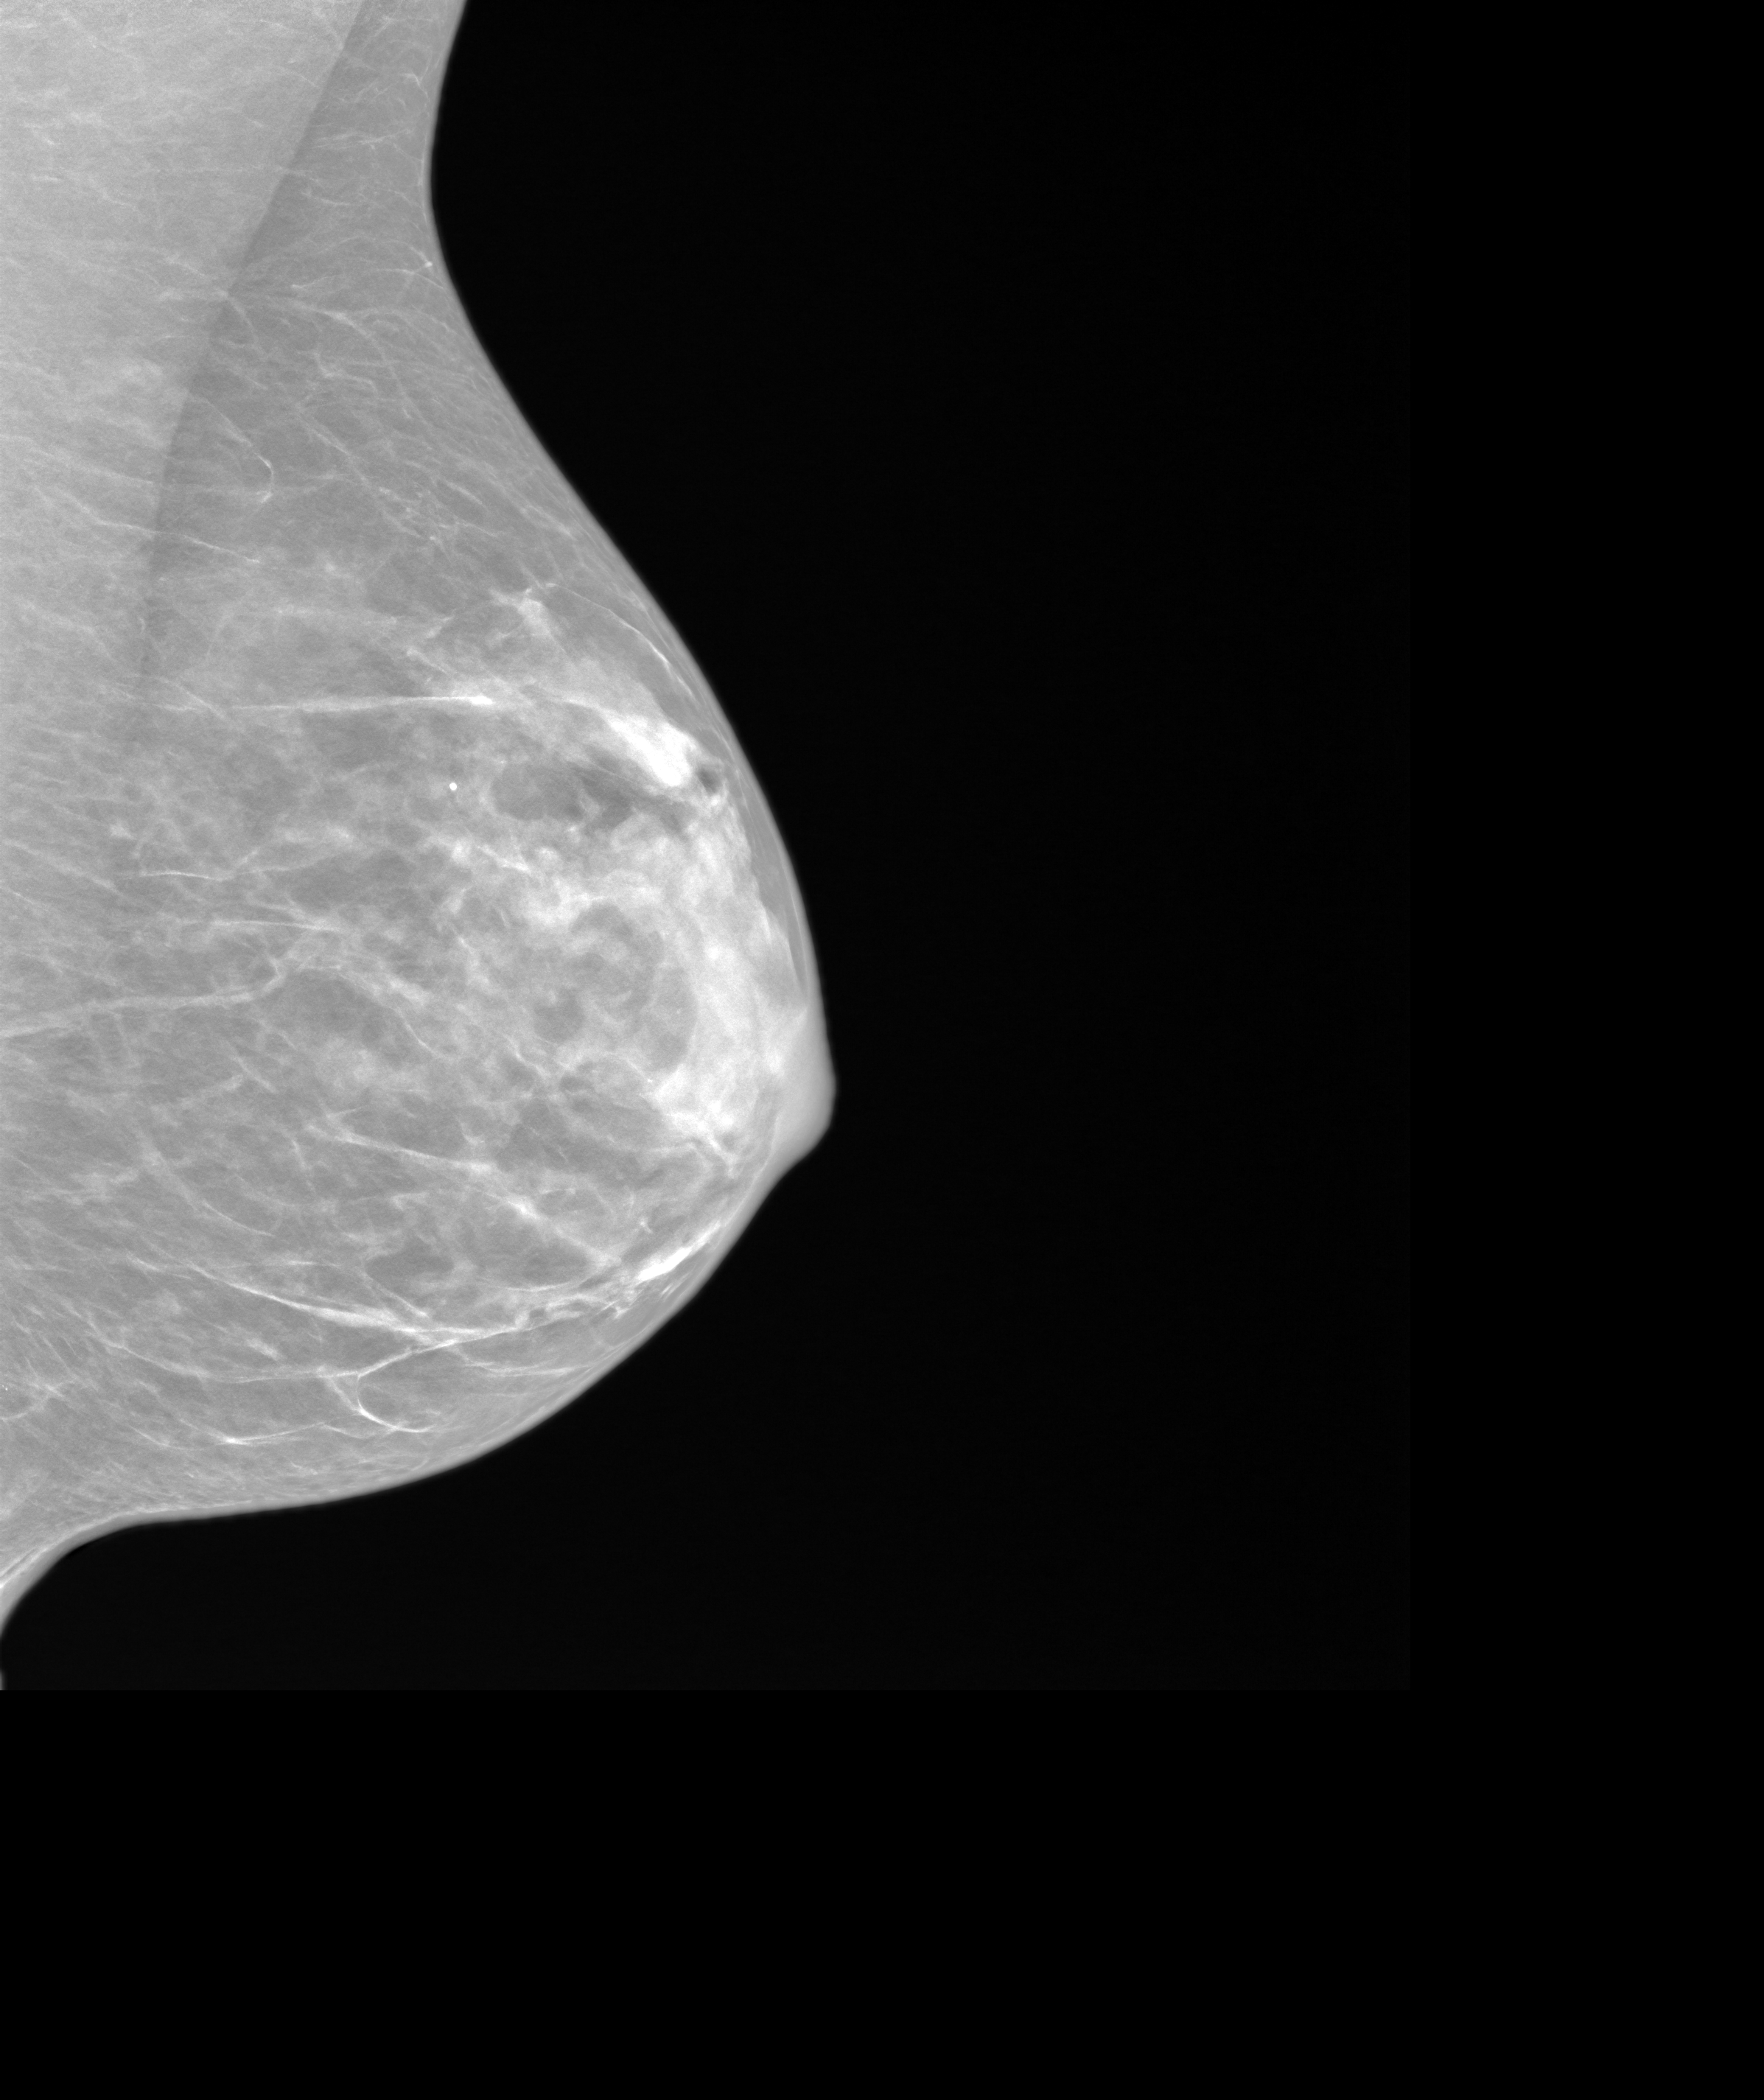
Synthetic 2-D view generated from a tomosynthesis acquisition (not an FFDM exposure); left breast; mediolateral oblique (MLO) view; annual screening mammography examination. Patient aged 43 years (female).
- breast density at the screening exam (both breasts): heterogeneously dense (BI-RADS density category c)
- final BI-RADS category for the screening round (tomosynthesis exam, both breasts): category 1
- recall: no recall after this screen